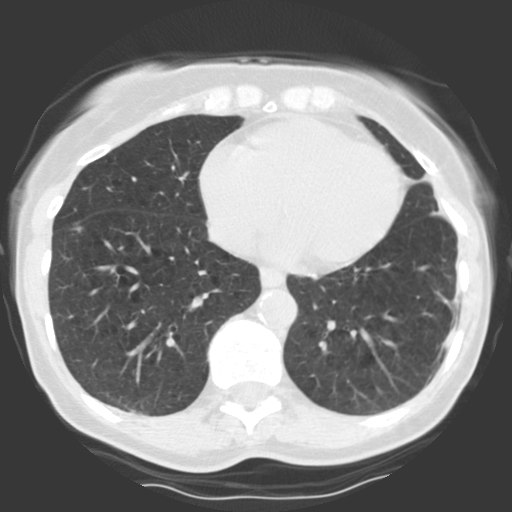
Axial slice from a low-dose chest CT screening exam. Baseline screening round. Lung window (W 1500 / L -600 HU). Female participant, aged 68 years at enrolment.
Expert reader's lesion annotation, box from (x=59, y=209) to (x=96, y=248) px. The screening reader recorded 2 non-calcified nodules or masses ≥4 mm on this exam (right lower lobe, right middle lobe); which of them this box marks is not recorded. Later outcome: lung cancer diagnosed 40 days after this screen — bronchiolo-alveolar adenocarcinoma, NOS, right upper lobe, right middle lobe, right lower lobe, well differentiated (G1), stage IV (AJCC 6th edition).